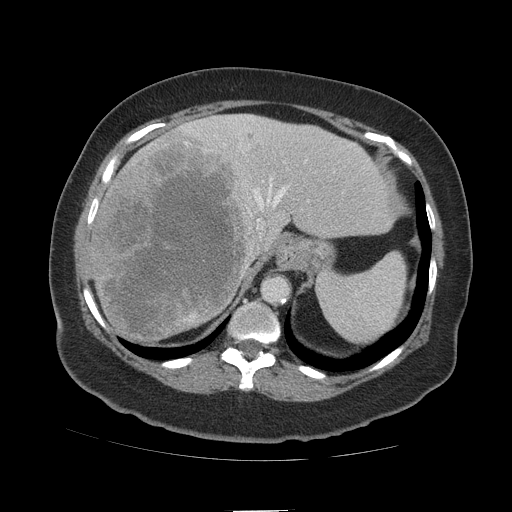
Contrast-enhanced abdominal CT (liver protocol), one axial slice; position 82 of 109 along the scan axis; reconstruction kernel STANDARD; 140 kVp; soft-tissue window (W 400 / L 40 HU); 2.5 mm slice thickness; 512 × 512 image matrix, field of view 420 × 420 mm. Case-level facts recorded for this patient, not image findings: diagnosis: hepatocellular carcinoma (patient treated with transarterial chemoembolisation; whether this scan precedes or follows treatment is not stated here); TNM stage (as recorded): Stage-IVB; Child-Pugh class: A; tumour differentiation: poorly differentiated; tumour nodularity: multinodular.
Structures marked on this image (semi-automatically segmented with operator editing):
- liver parenchyma outside the tumour (the mass and vessels are separate outlines, so this box may not span the whole liver): bounding box (x1, y1, x2, y2) in pixels: (86, 114, 398, 340)
- mass: (92, 131, 267, 340)
- liver vessels: (182, 117, 350, 221)